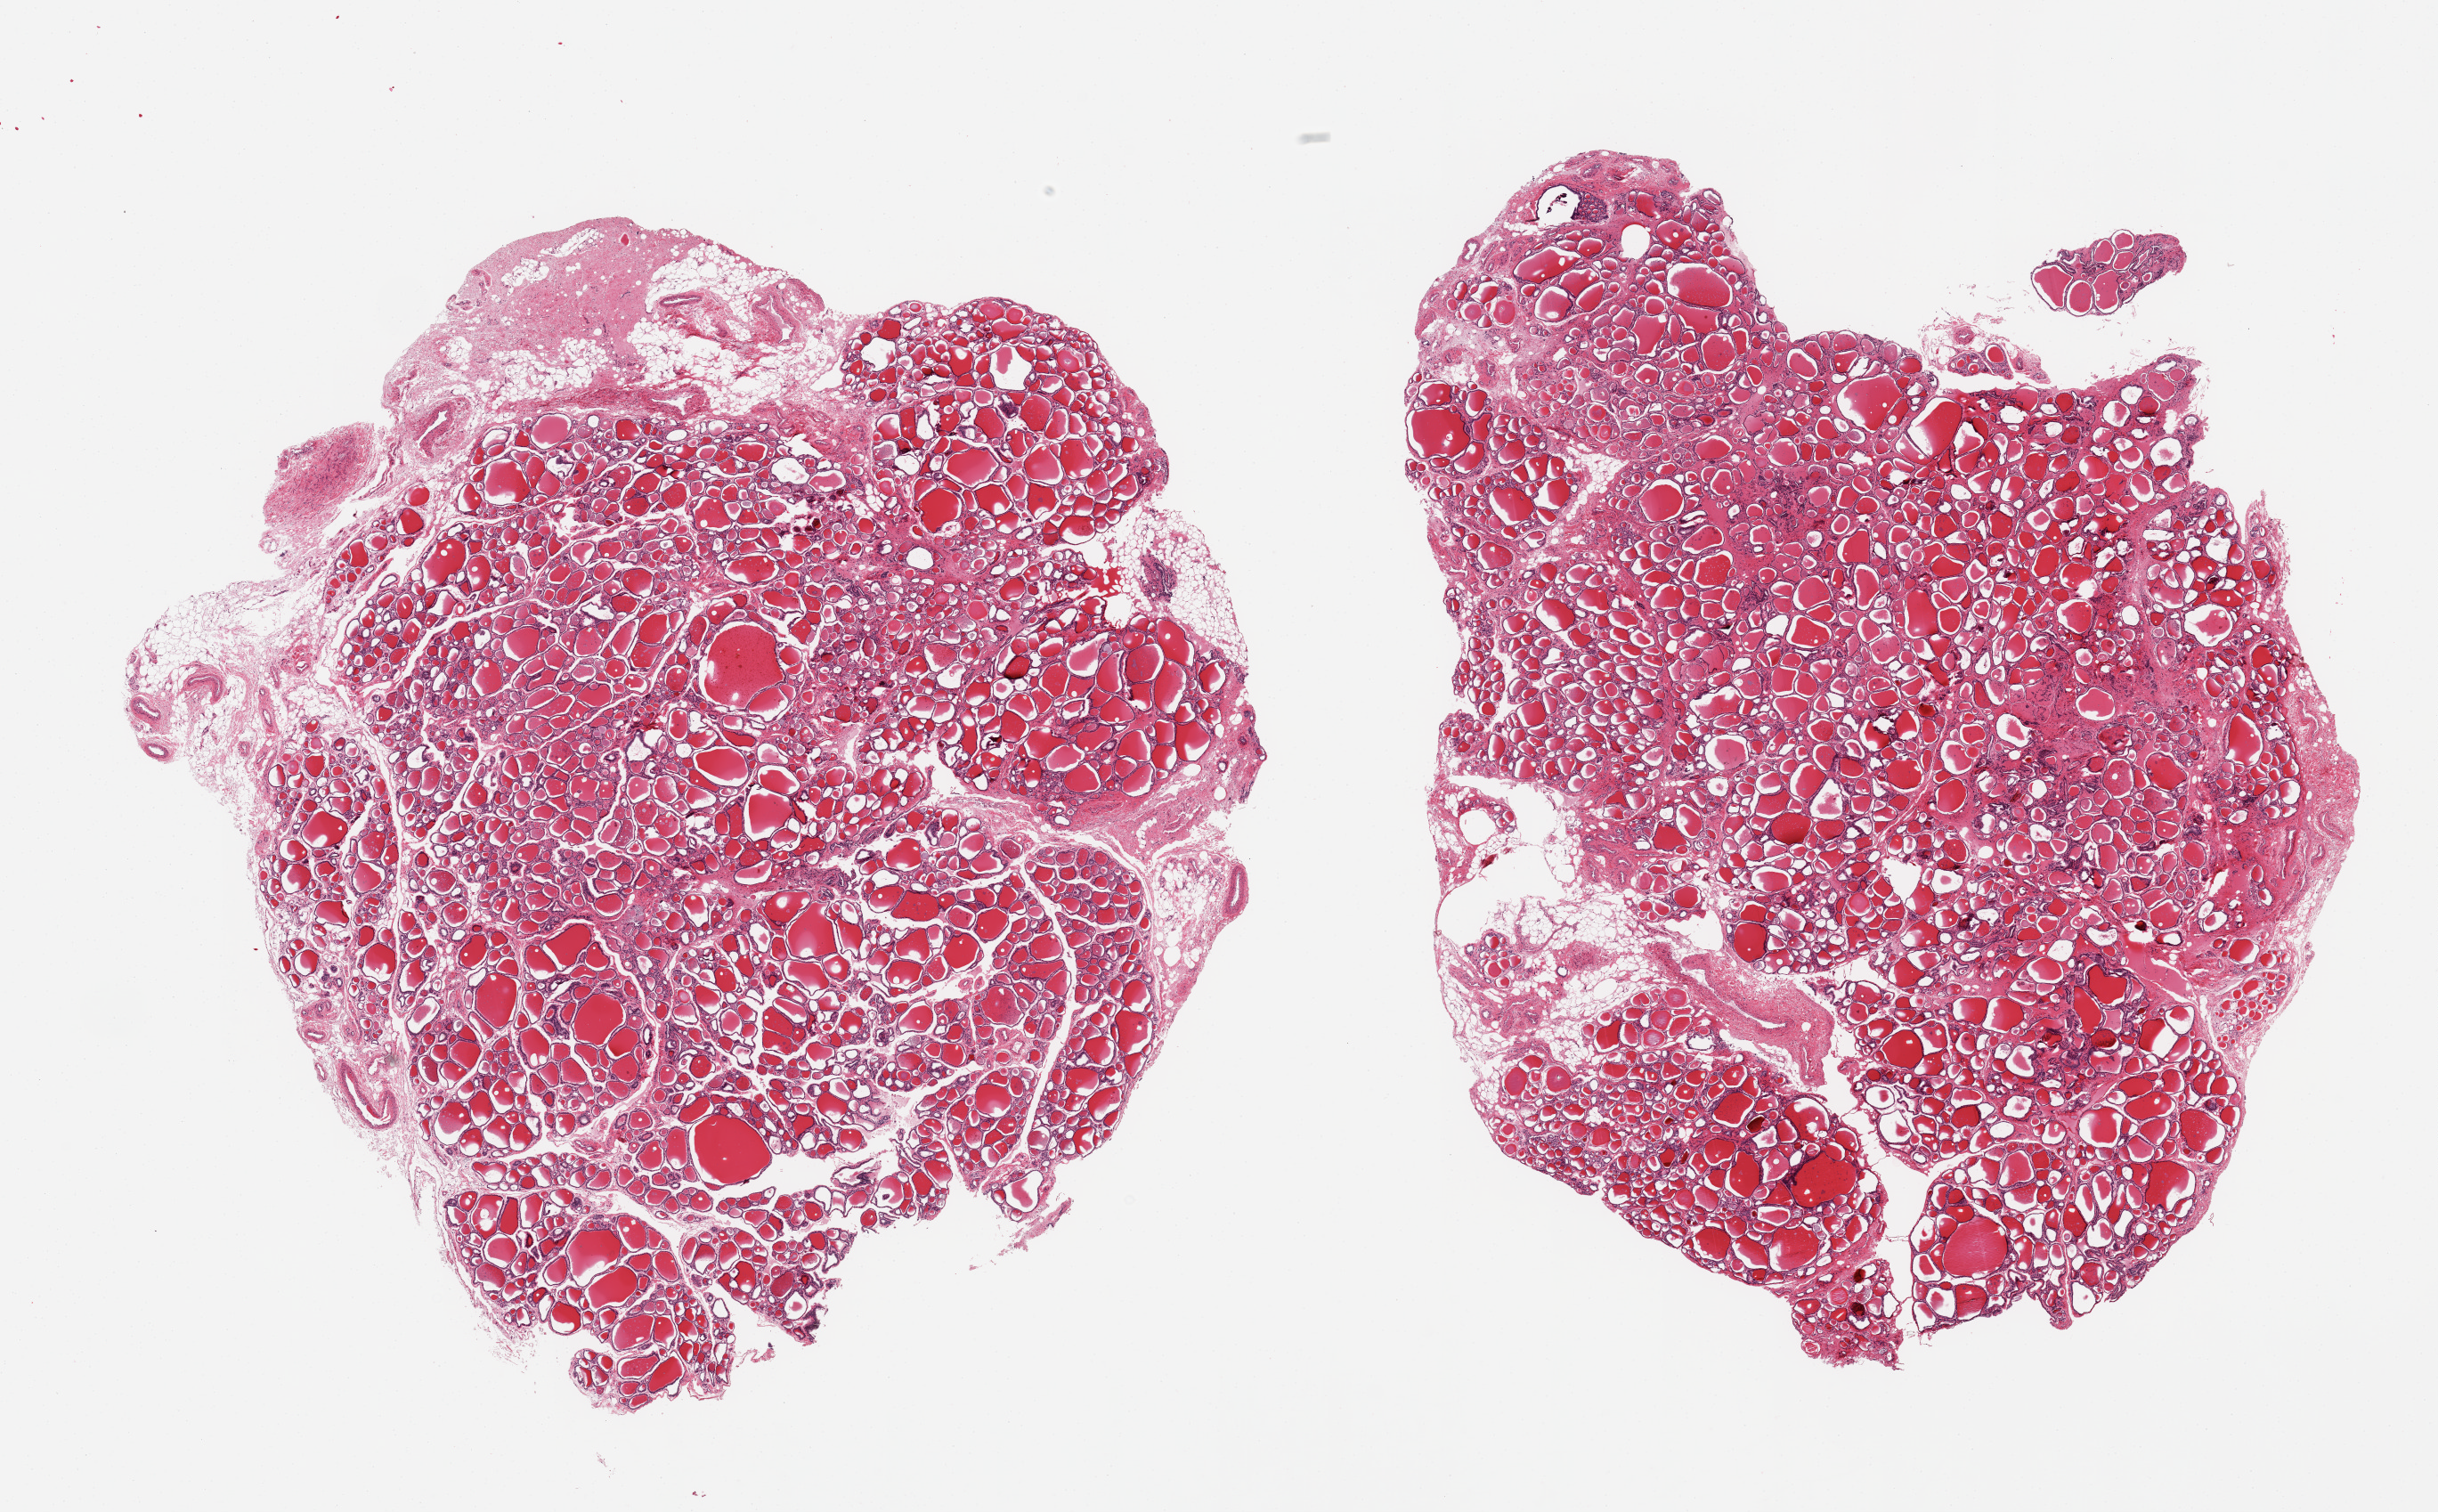
Digitized hematoxylin and eosin (H&E)-stained section, shown as a low-resolution overview of the whole scanned area (about 21.7 x 13.4 mm, slide scanned at 20x), PAXgene-fixed paraffin-embedded (PFPE) section, section of thyroid (target tissue), tissue donor sample. Donor: female.
- review note (as recorded): 2 pieces; 10% external fibrofatty tissue